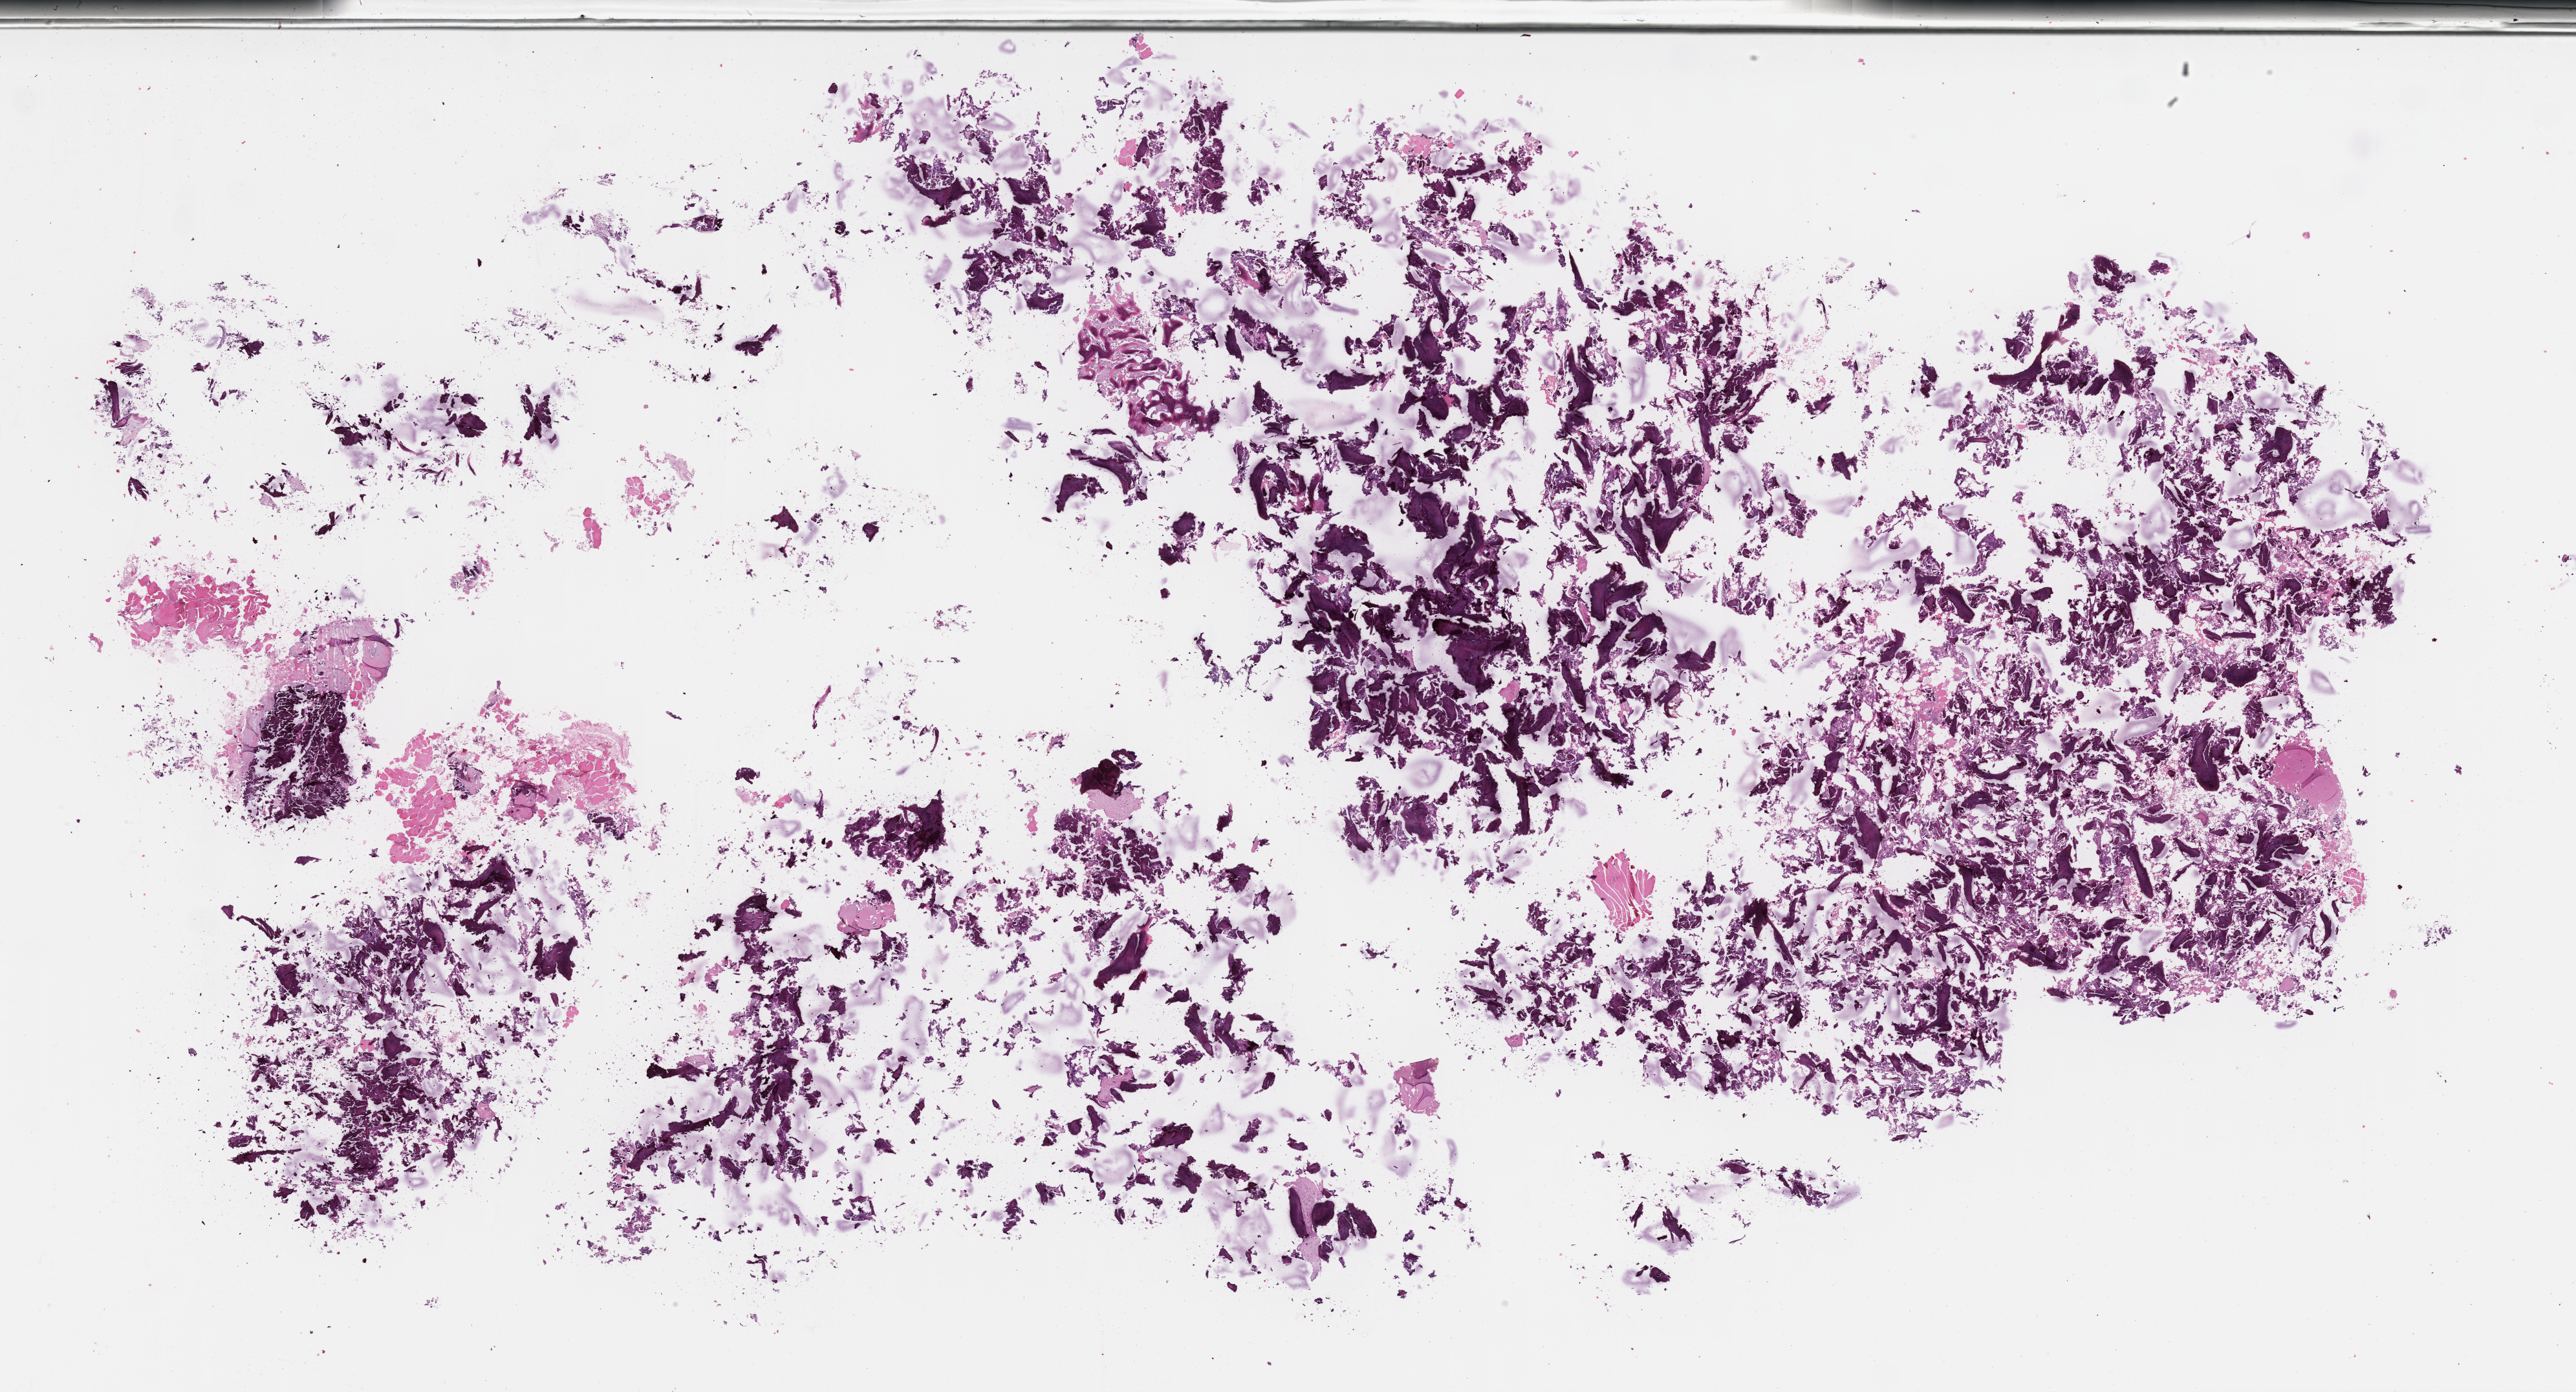
Digitized H&E-stained section — low-resolution overview of the scanned area, about 32.2 x 17.4 mm; formalin-fixed paraffin-embedded section; archival tissue. Patient: female.
This section: metastasis (sampled organ not recorded). Primary diagnosis of the patient: Invasive Breast Carcinoma.